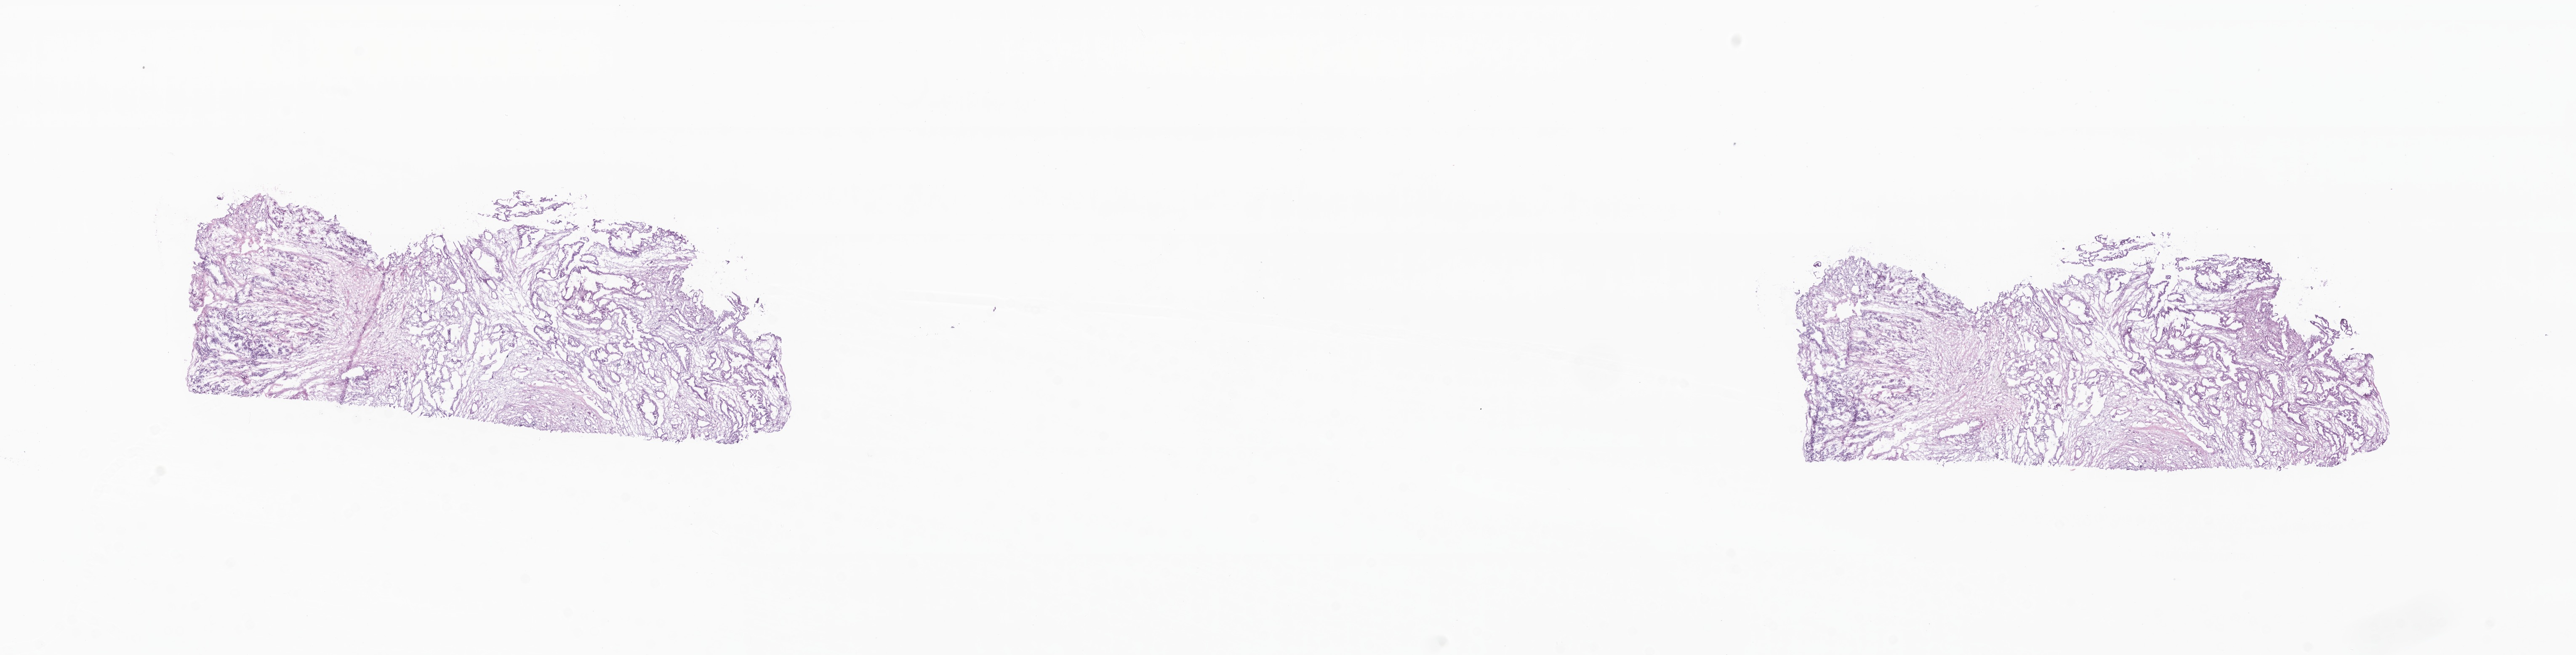
Digitized haematoxylin and eosin-stained section, shown as a low-resolution overview of the whole scanned area (about 25.8 x 6.6 mm); cryosection; primary tumor; anatomic site: tail of pancreas. Female, age 62 years at initial diagnosis. Composition of this section per pathologist review: tumor cells 30%, tumor nuclei 40%.
Diagnosis: Infiltrating duct carcinoma, NOS.